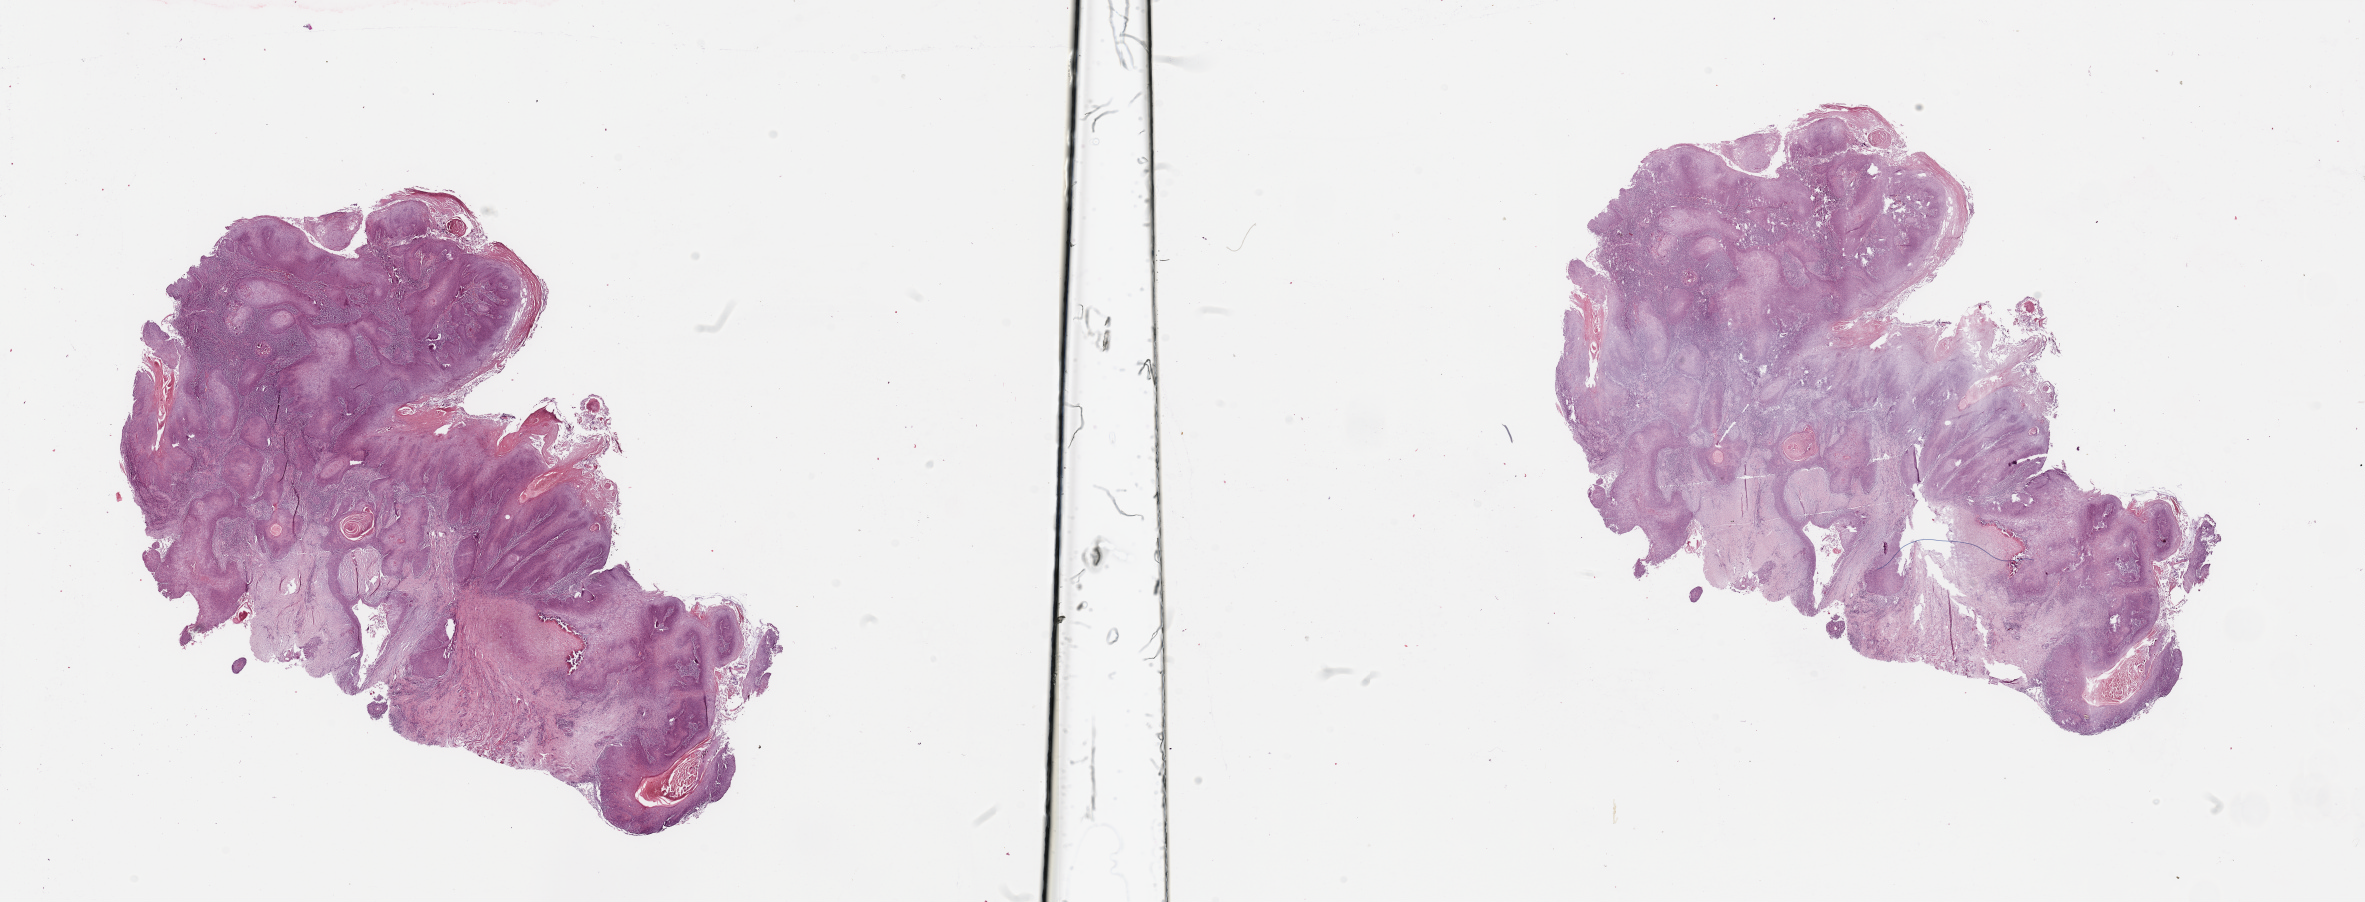
H&E whole-slide image — shown as a low-resolution overview of the whole scanned area (about 37.4 x 14.3 mm), head and neck, tissue type not recorded. Patient: male, age 61 years.
Patient diagnosis: Squamous cell carcinoma, NOS (larynx, NOS).